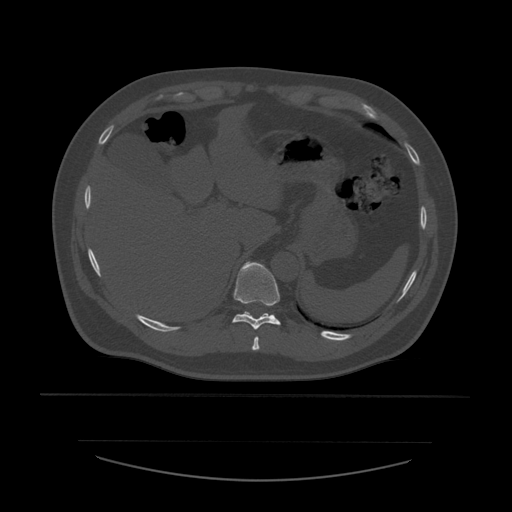
CT including the spine, one axial slice. Slice 295 of 532 in the series (ordered by position). Reconstruction kernel STANDARD. 120 kVp. Bone window (W 1800 / L 400 HU). 1.25 mm slice thickness. 512 × 512 image matrix, field of view 441 × 441 mm. Patient age 44 years. Case-level facts recorded for this patient, not image findings: primary cancer: soft tissue sarcoma.
Structures marked on this image (semi-automatic segmentation, software-assisted and operator-edited):
- T10 vertebra: bounding box [x1, y1, x2, y2] px = [232, 262, 281, 330]
- T9 vertebra: [252, 337, 260, 351]